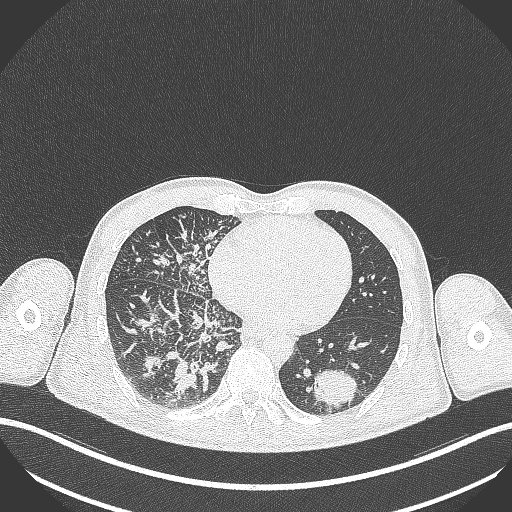
Chest CT, one axial slice; slice 112 of 348 in the series (ordered by position); reconstruction kernel B70f; lung window (W 1500 / L -600 HU); 1 mm slice thickness; 512 × 512 image matrix, field of view 400 × 400 mm. Male patient, age 49 years. From the clinical record (not read from this slice): clinical TNM (as recorded): T2b N1 M0.
Outlined on this slice (bounding box drawn by a radiologist):
- lung tumour (recorded histology: adenocarcinoma): bounding box [x1, y1, x2, y2] px = [306, 366, 360, 407]